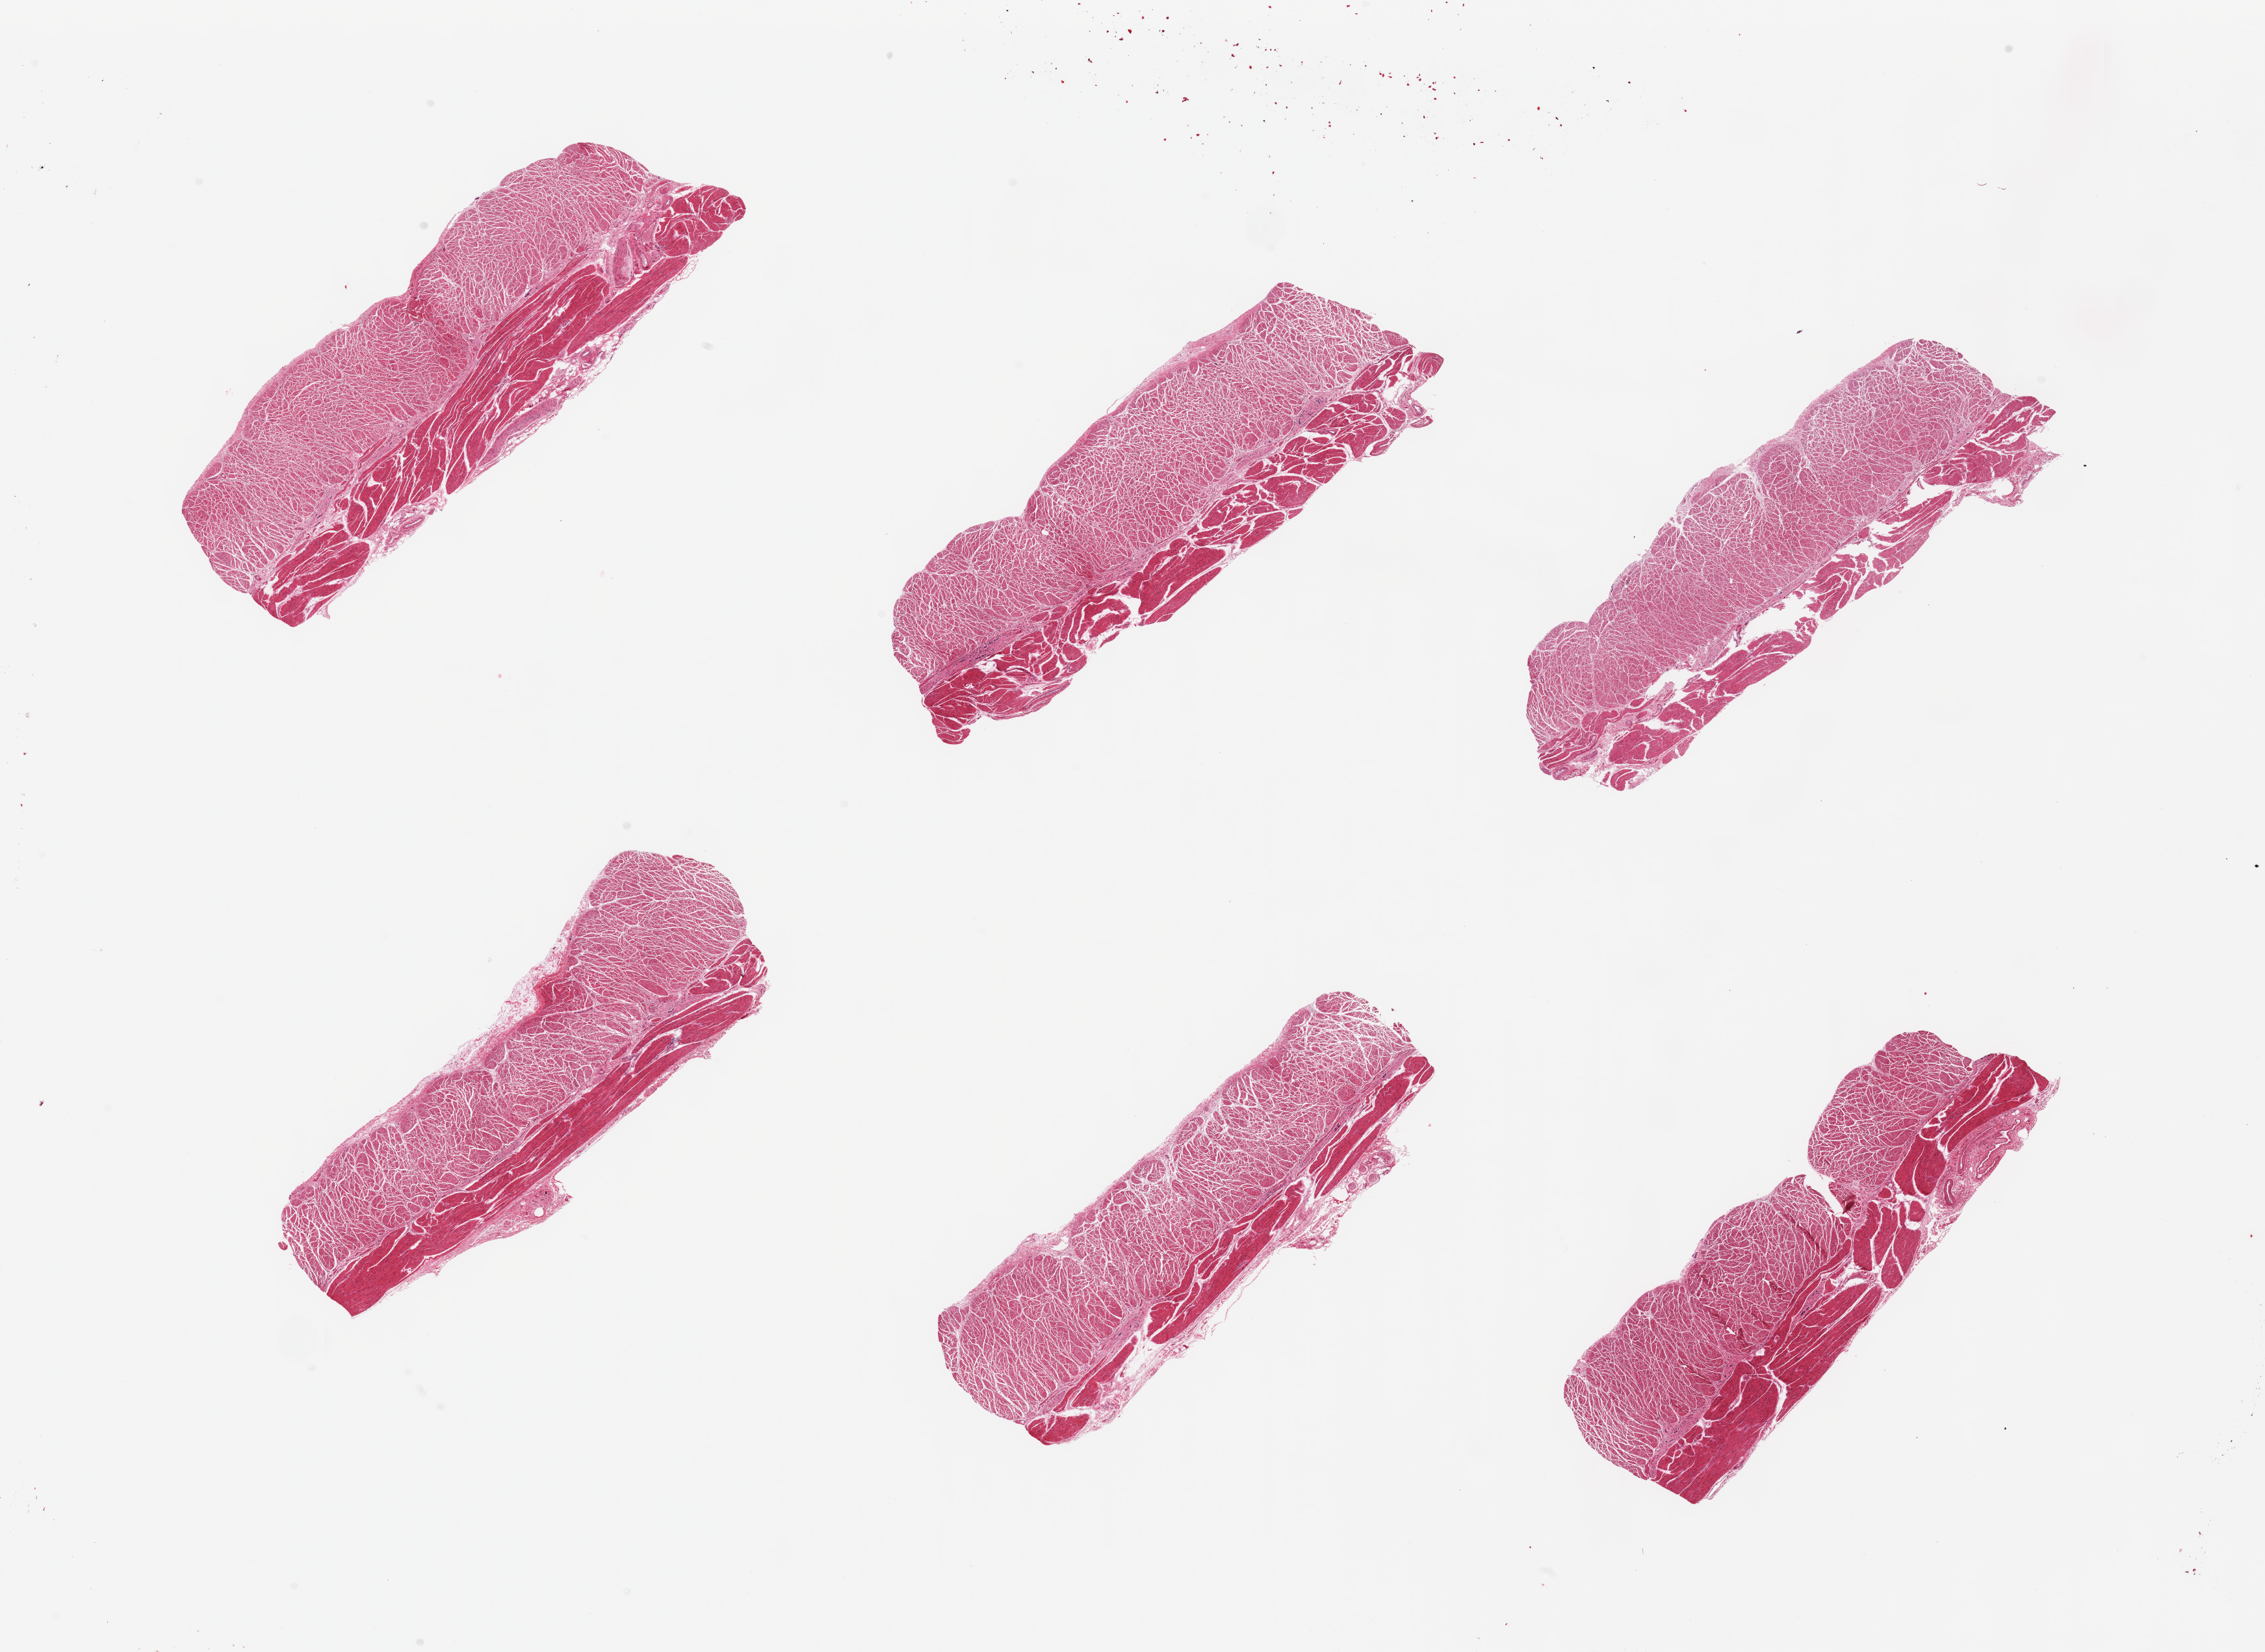
Hematoxylin and eosin (H&E) whole-slide image — whole scanned area (about 27.6 x 20.1 mm) shown as a low-resolution overview. PAXgene-fixed paraffin-embedded (PFPE) section. Section of esophageal muscle (target tissue). Donor tissue sample. Female donor.
- review note (as recorded): 6 pieces; well trimmed muscularis